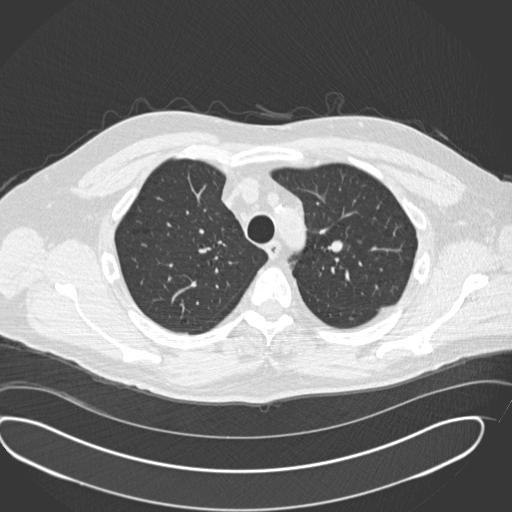
Chest CT (low-dose screening protocol), one axial image. Second annual screen. Lung window (W 1500 / L -600 HU). Standard (soft-tissue) reconstruction kernel (B30f). Slice 47 of 190 in the series. 512 × 512 image matrix, field of view 418 × 418 mm. Male participant, aged 56 years at enrolment. Current smoker at enrolment.
• Lesion marked by an expert reader, bounding box <312,225,368,270> (left, top, right, bottom; pixels).
• Screening reader's record for this exam: no non-calcified nodule ≥4 mm recorded.
• Later outcome: lung cancer diagnosed 520 days after this screen (after the third annual screen) — neuroendocrine carcinoma, NOS, left upper lobe, well differentiated (G1), stage IA (AJCC 6th edition), 20 mm at pathology.